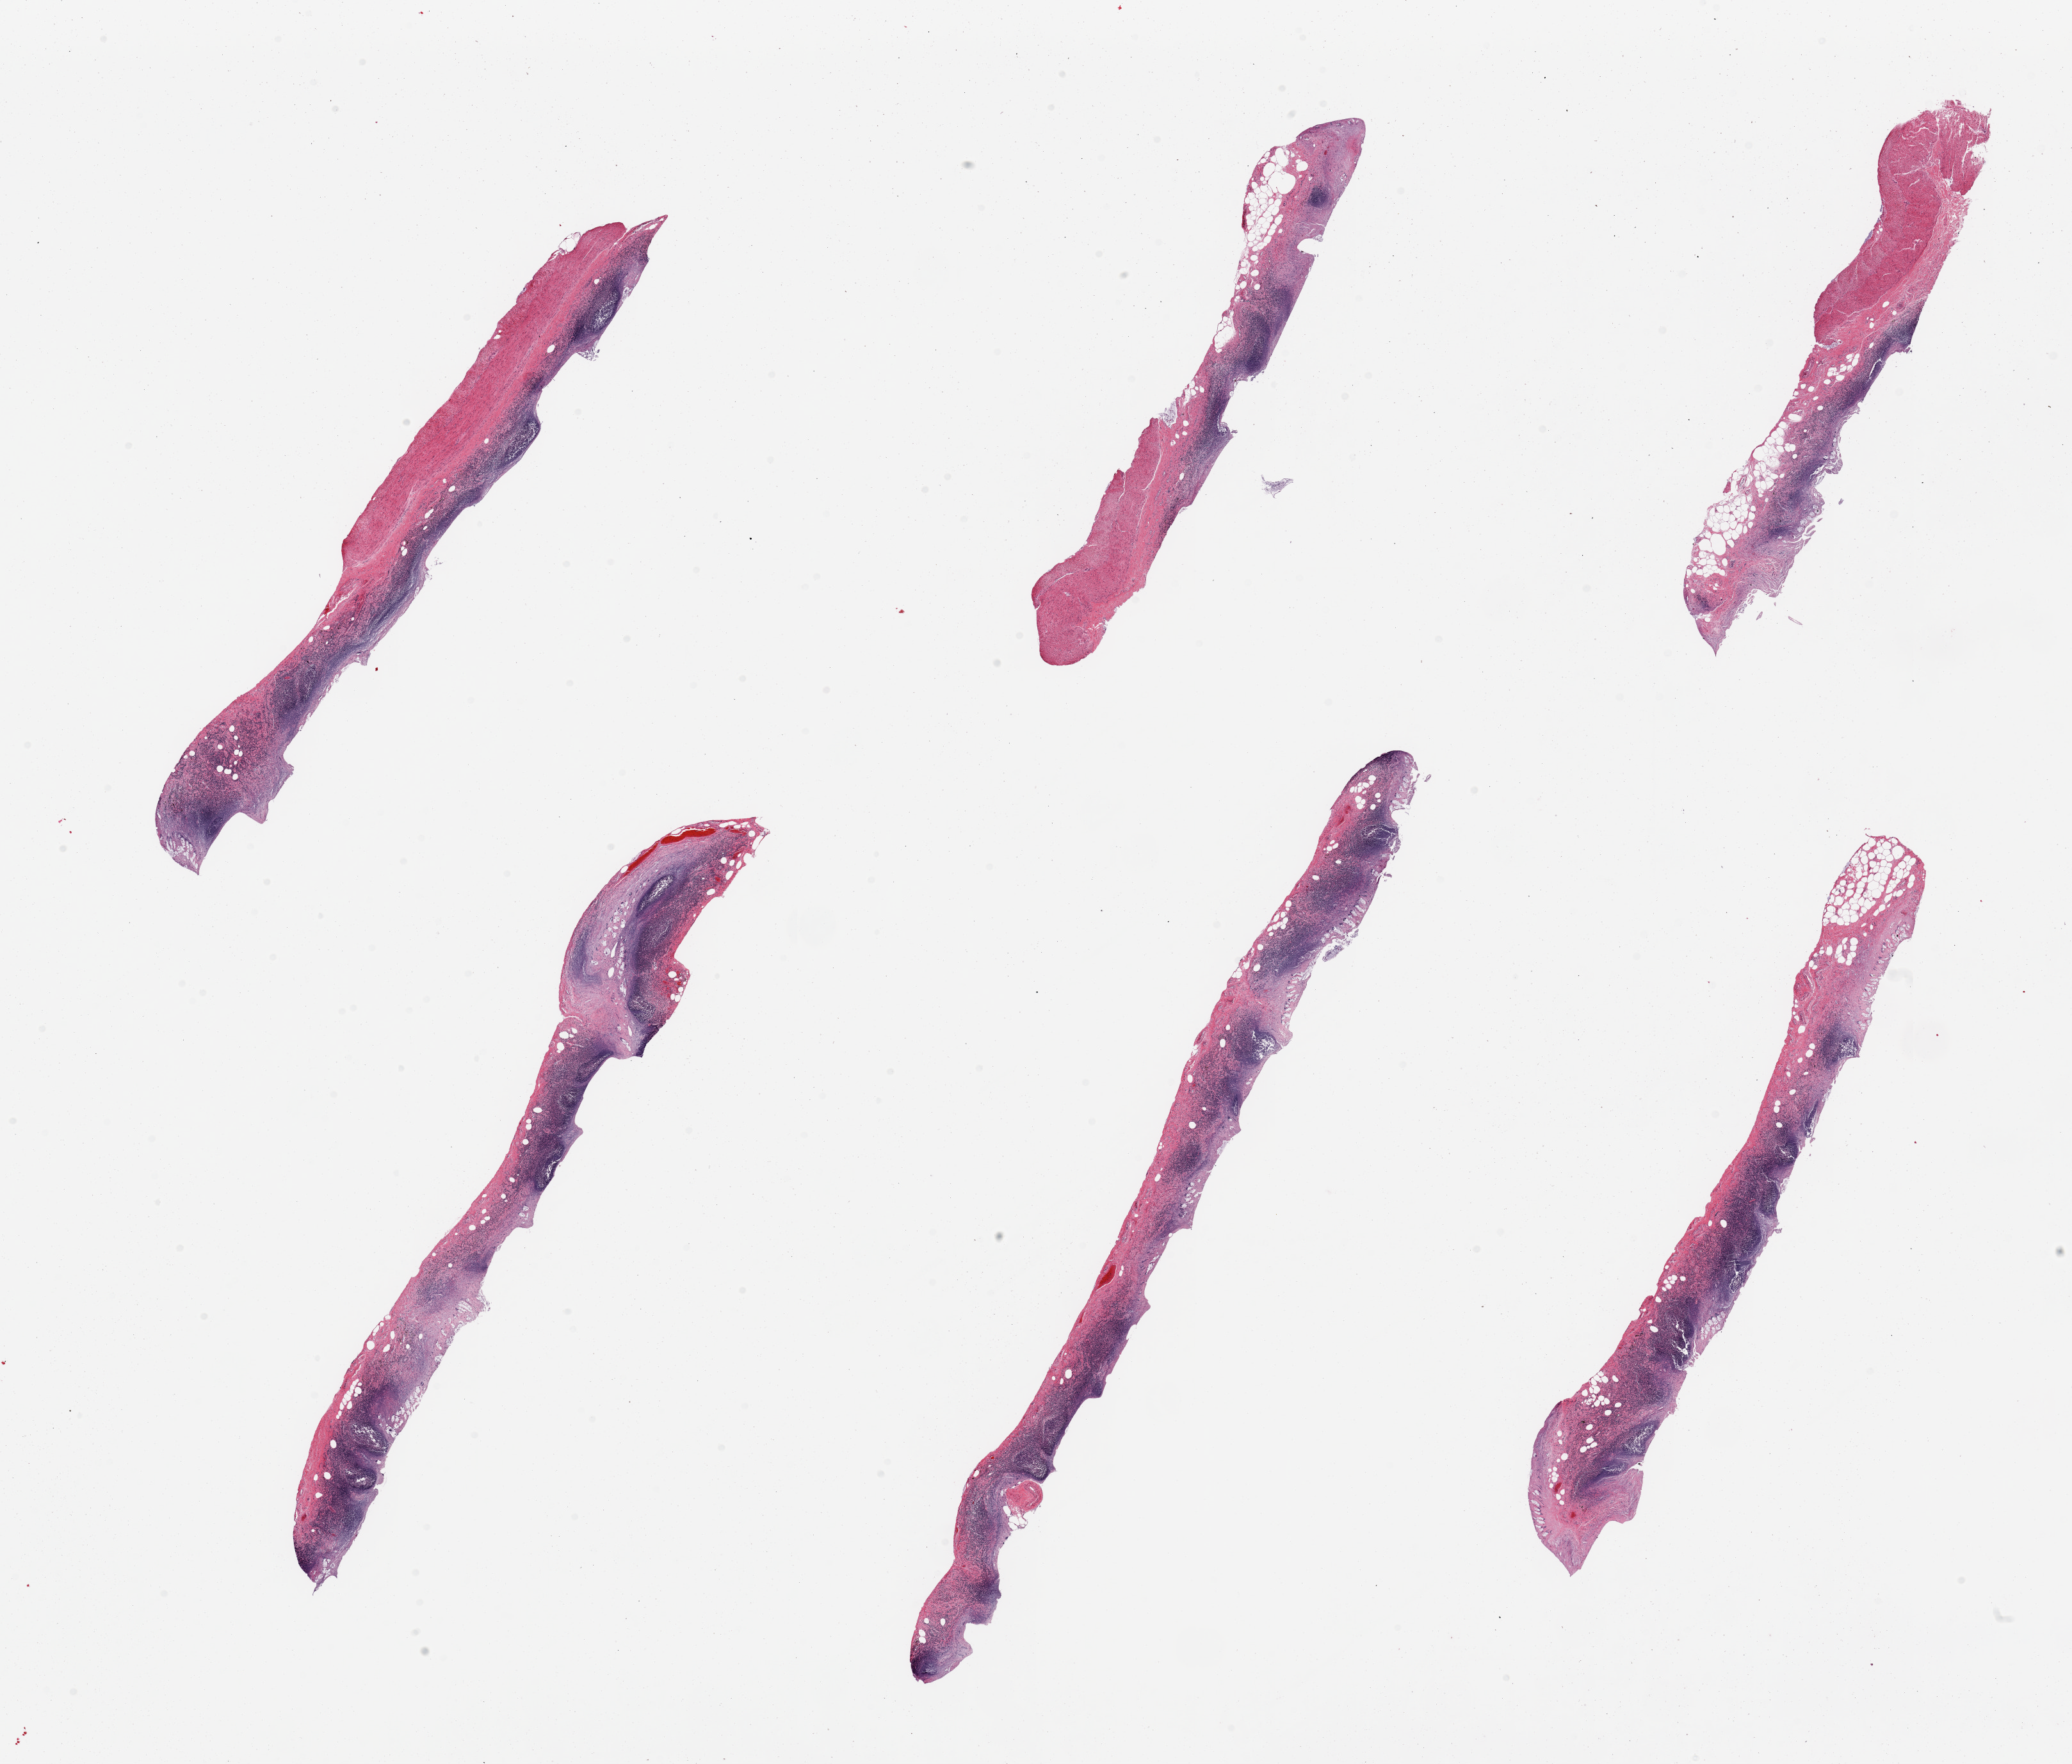
Whole-slide image, H&E stain, brightfield, low-resolution overview of the scanned area, about 25.6 x 21.8 mm (from a 20x scan), PAXgene-fixed paraffin-embedded (PFPE) section, target tissue: ileum, donor tissue sample. Donor sex: male.
Review note (as recorded): 6 pieces; mucosa autolyzed, but abundant lymphoid tissue still intact; well dissected.